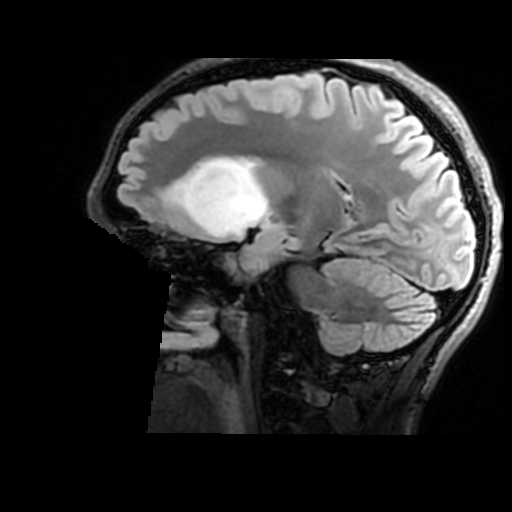
Brain MRI from a brain-tumour surgery series, one sagittal slice; position 104 of 176 along the scan axis; T2 FLAIR; 1 mm slice thickness; 512 × 512 image matrix. From the clinical record (not read from this slice): histopathology: Astrocytoma; WHO grade: 2.
Structures marked on this image (outlined manually by an expert reader):
- tumour: box from (x=169, y=157) to (x=273, y=237) px